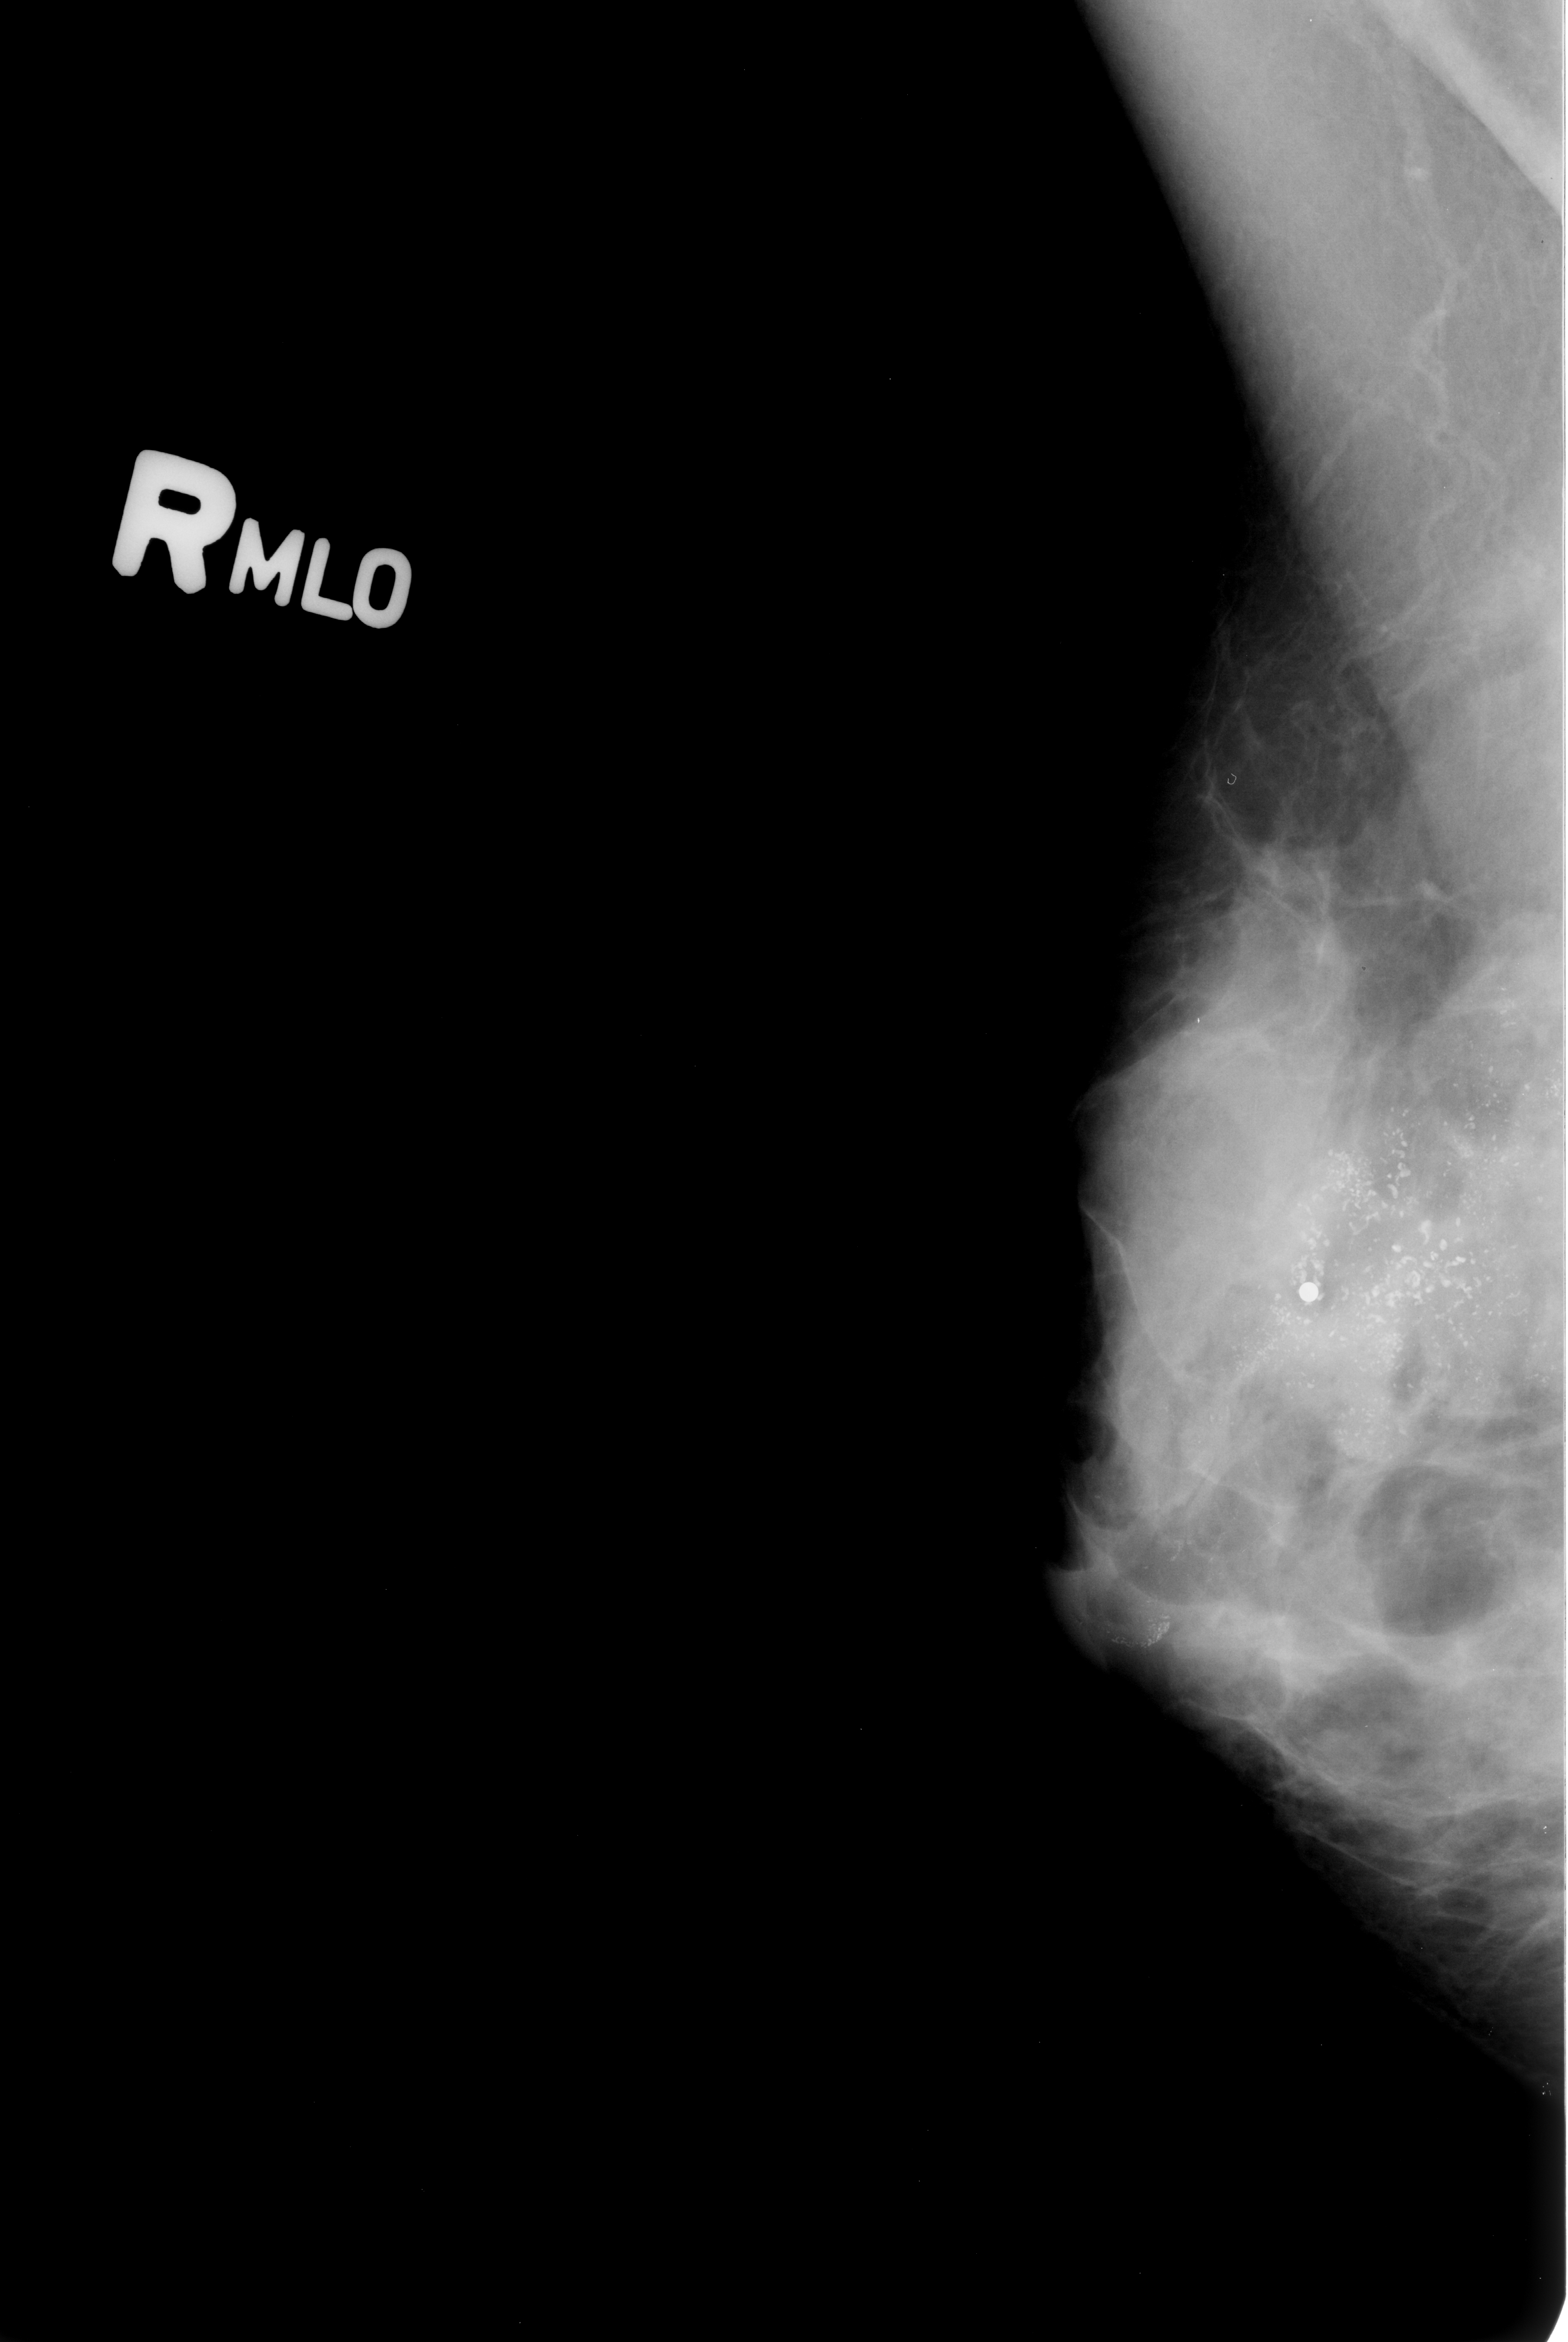
Scanned film-screen mammogram; right breast; mediolateral oblique (MLO) view; 1568 × 2342 image matrix.
Marked abnormalities (boxes around the expert regions of interest):
- calcifications, morphology pleomorphic, distribution regional; BI-RADS assessment category 5; pathology result (as recorded, not read from the image): malignant: bounding box [x1, y1, x2, y2] px = [1075, 1015, 1561, 1663]